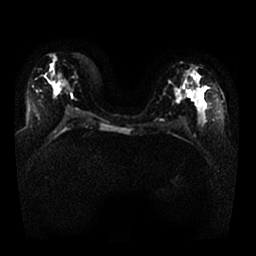
Breast MRI, one axial slice. Position 13 of 25 along the scan axis. Diffusion-weighted series; image 2 of 4 stored at this slice position (different b-values; order by instance number). 1.5 T. 4 mm slice thickness. 256 × 256 image matrix. Female patient.
Structures marked on this image (expert manual segmentation):
- tumour on diffusion-weighted imaging: box from (x=187, y=90) to (x=191, y=96) px